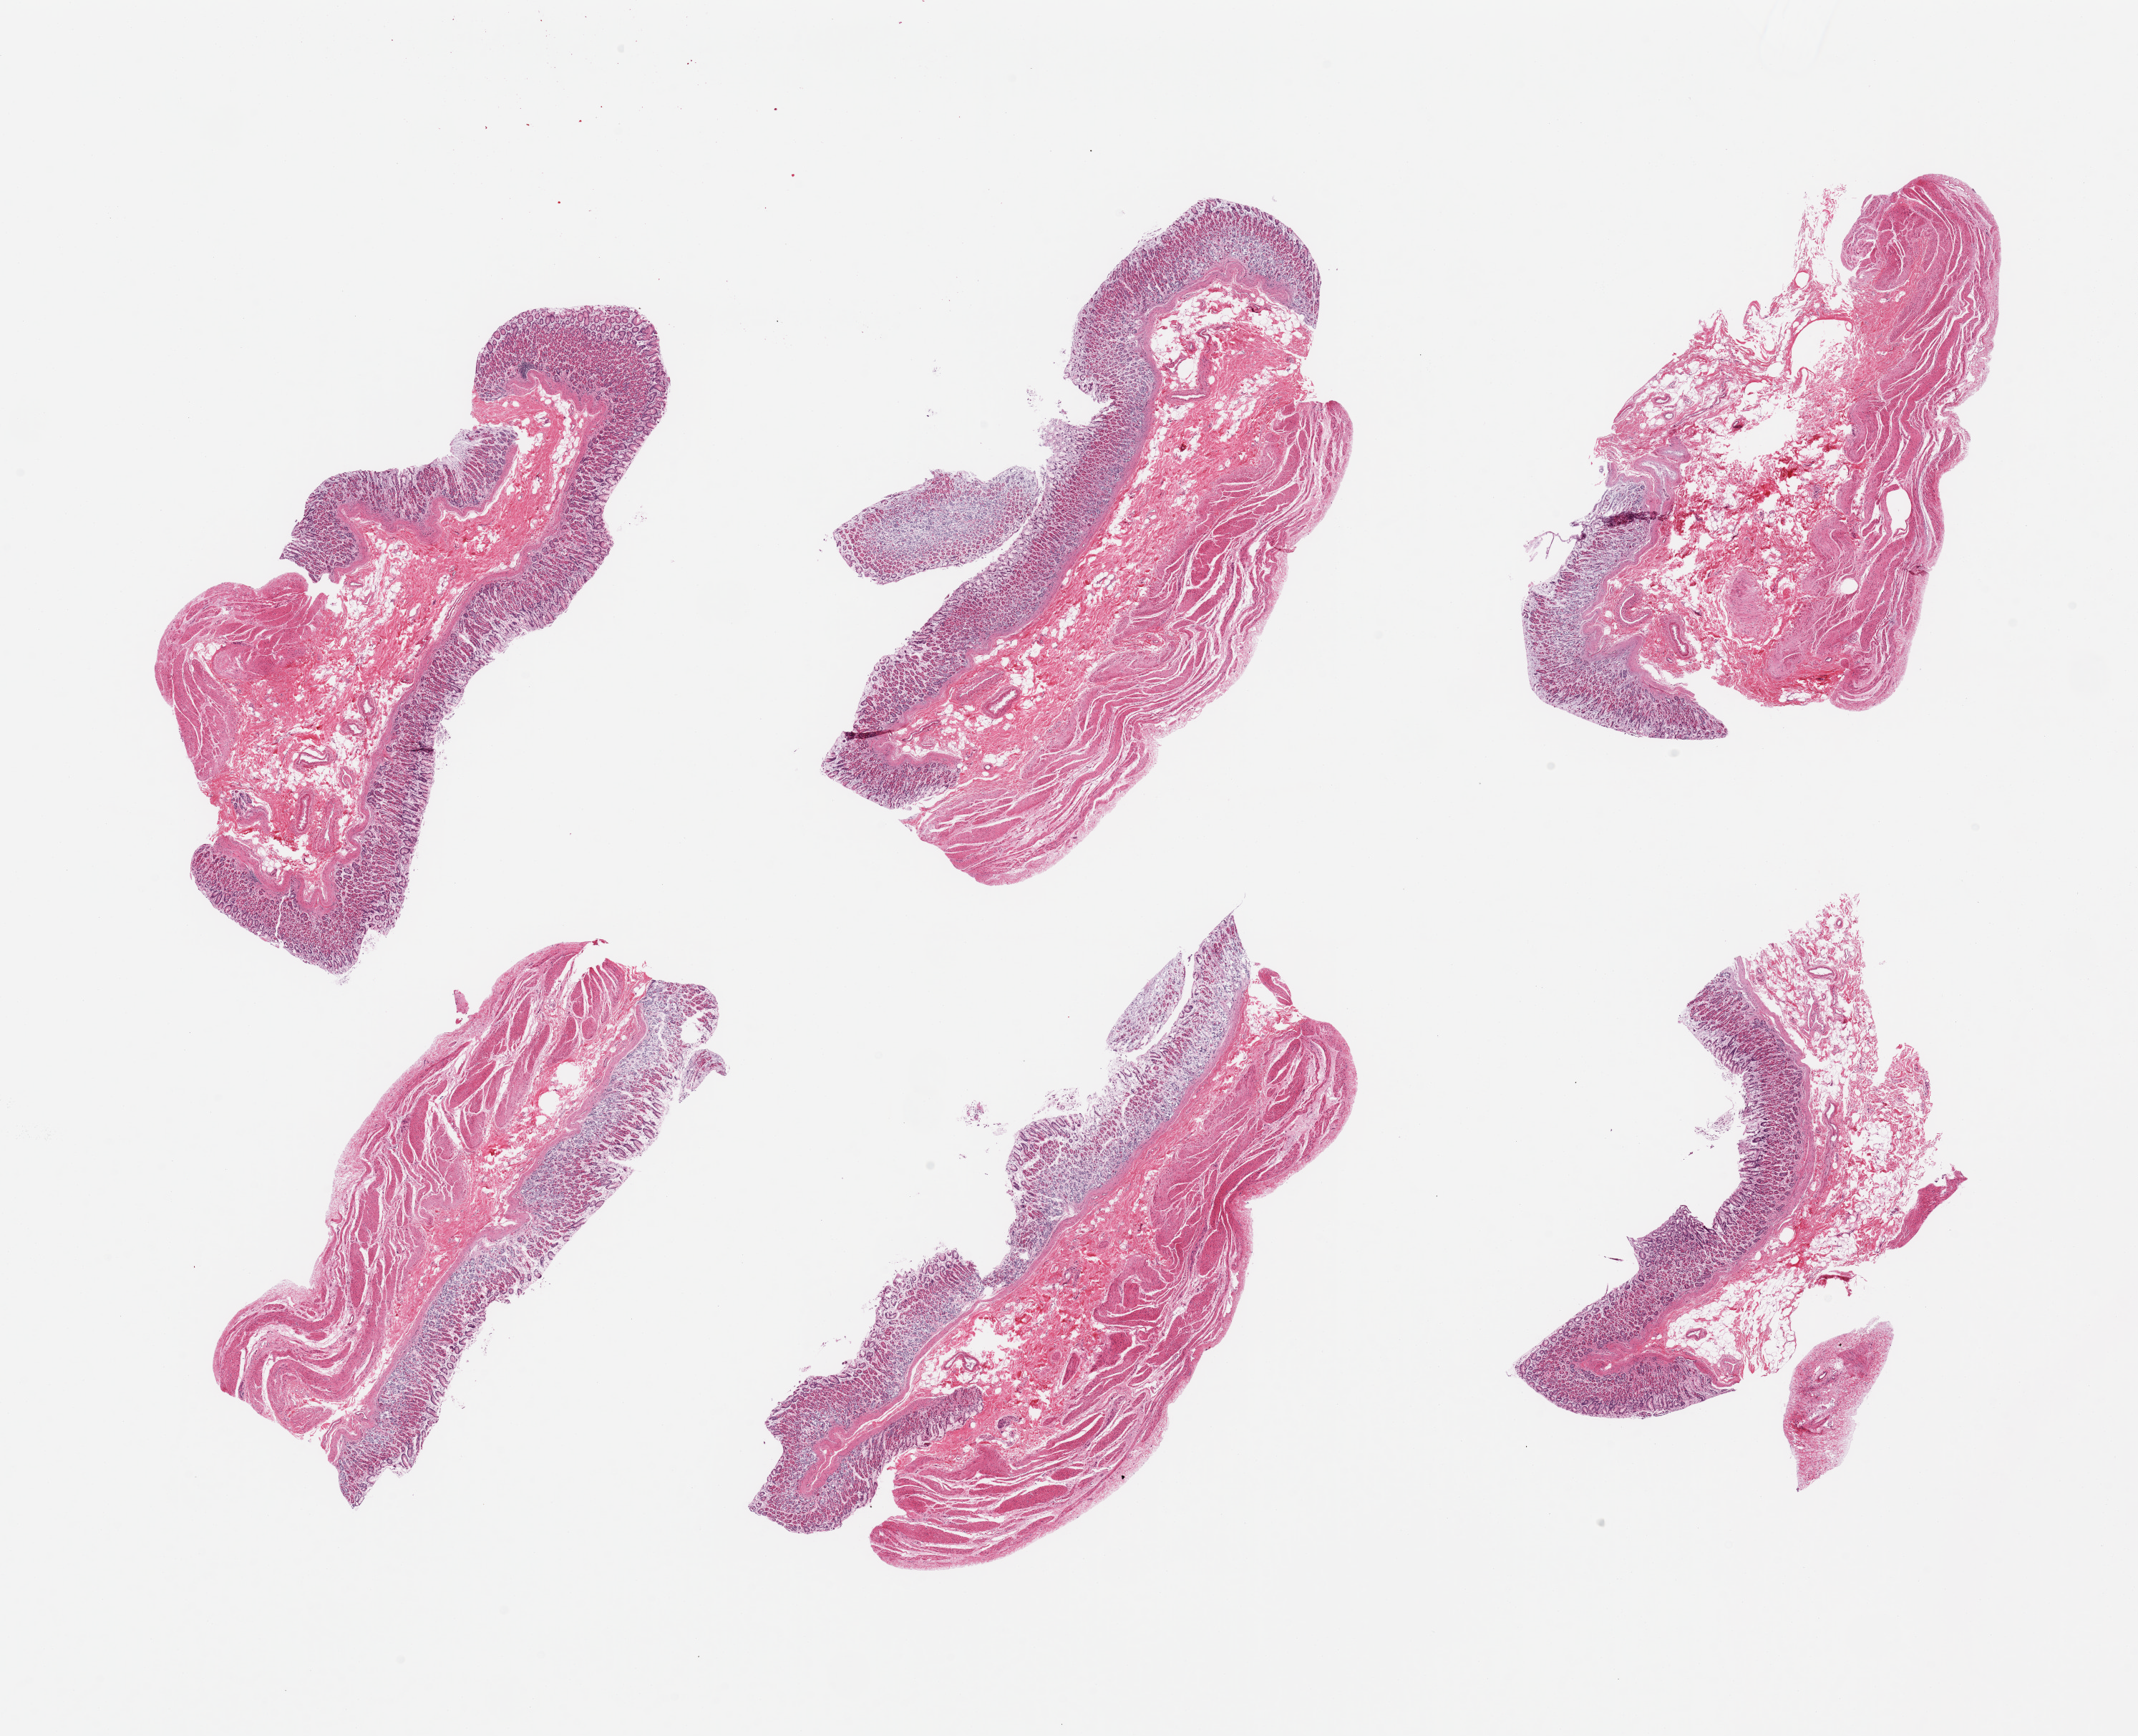
Hematoxylin and eosin (H&E) whole-slide image — whole scanned area (about 23.6 x 19.2 mm, acquisition: 20x scan) shown as a low-resolution overview, PAXgene-fixed, paraffin-embedded tissue, target tissue: stomach, tissue donor sample. Male donor.
Reviewer comment on this tissue sample: 6 pieces; target mucosa up to ~0.7mm, moderately advanced autolysis, ~20-30% of thickness.